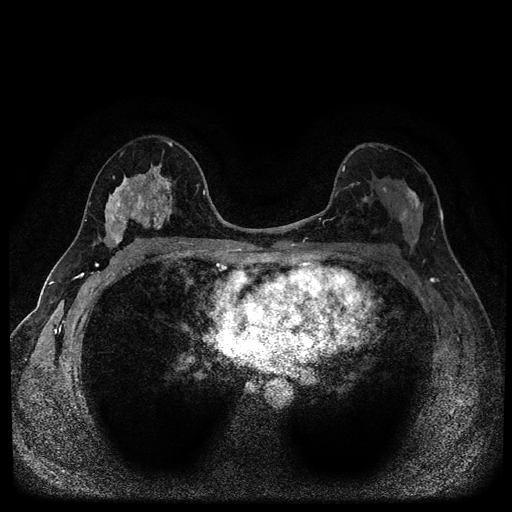
Breast MRI (dynamic contrast-enhanced, multi-phase), one axial slice; slice 58 of 116 in the series (ordered by position); dynamic contrast-enhanced series, time point 2 of 5 at this slice position (early post-contrast); 1.5 T; TE 2.7 ms, TR 5.4 ms; 2 mm slice thickness; 512 × 512 image matrix. Patient: female, 49 years.
Annotated regions visible in this slice (semi-automatic segmentation, software-assisted and operator-edited):
- breast lesion (labelled benign in the annotation): bounding box [x1, y1, x2, y2] px = [104, 165, 174, 248]